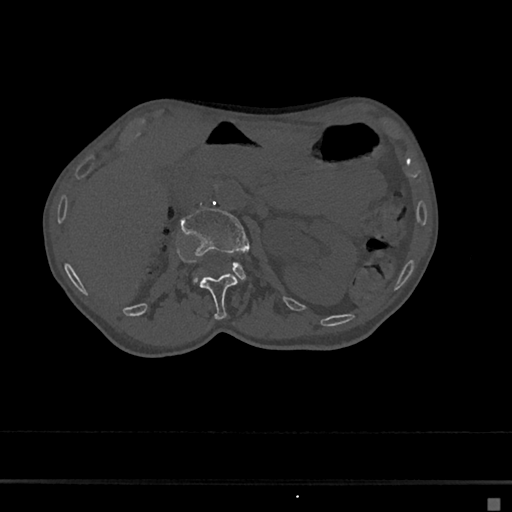
CT including the spine, one axial slice. Position 50 of 797 along the scan axis. Reconstruction kernel Br40s/3. Bone window (W 1800 / L 400 HU). 512 × 512 image matrix. Female patient, age 68 years. From the clinical record (not read from this slice): primary cancer: renal.
Annotated regions visible in this slice (semi-automatically segmented with operator editing):
- L1 vertebra: bounding box <199,273,237,320> (left, top, right, bottom; pixels)
- L2 vertebra: <181,208,250,279>